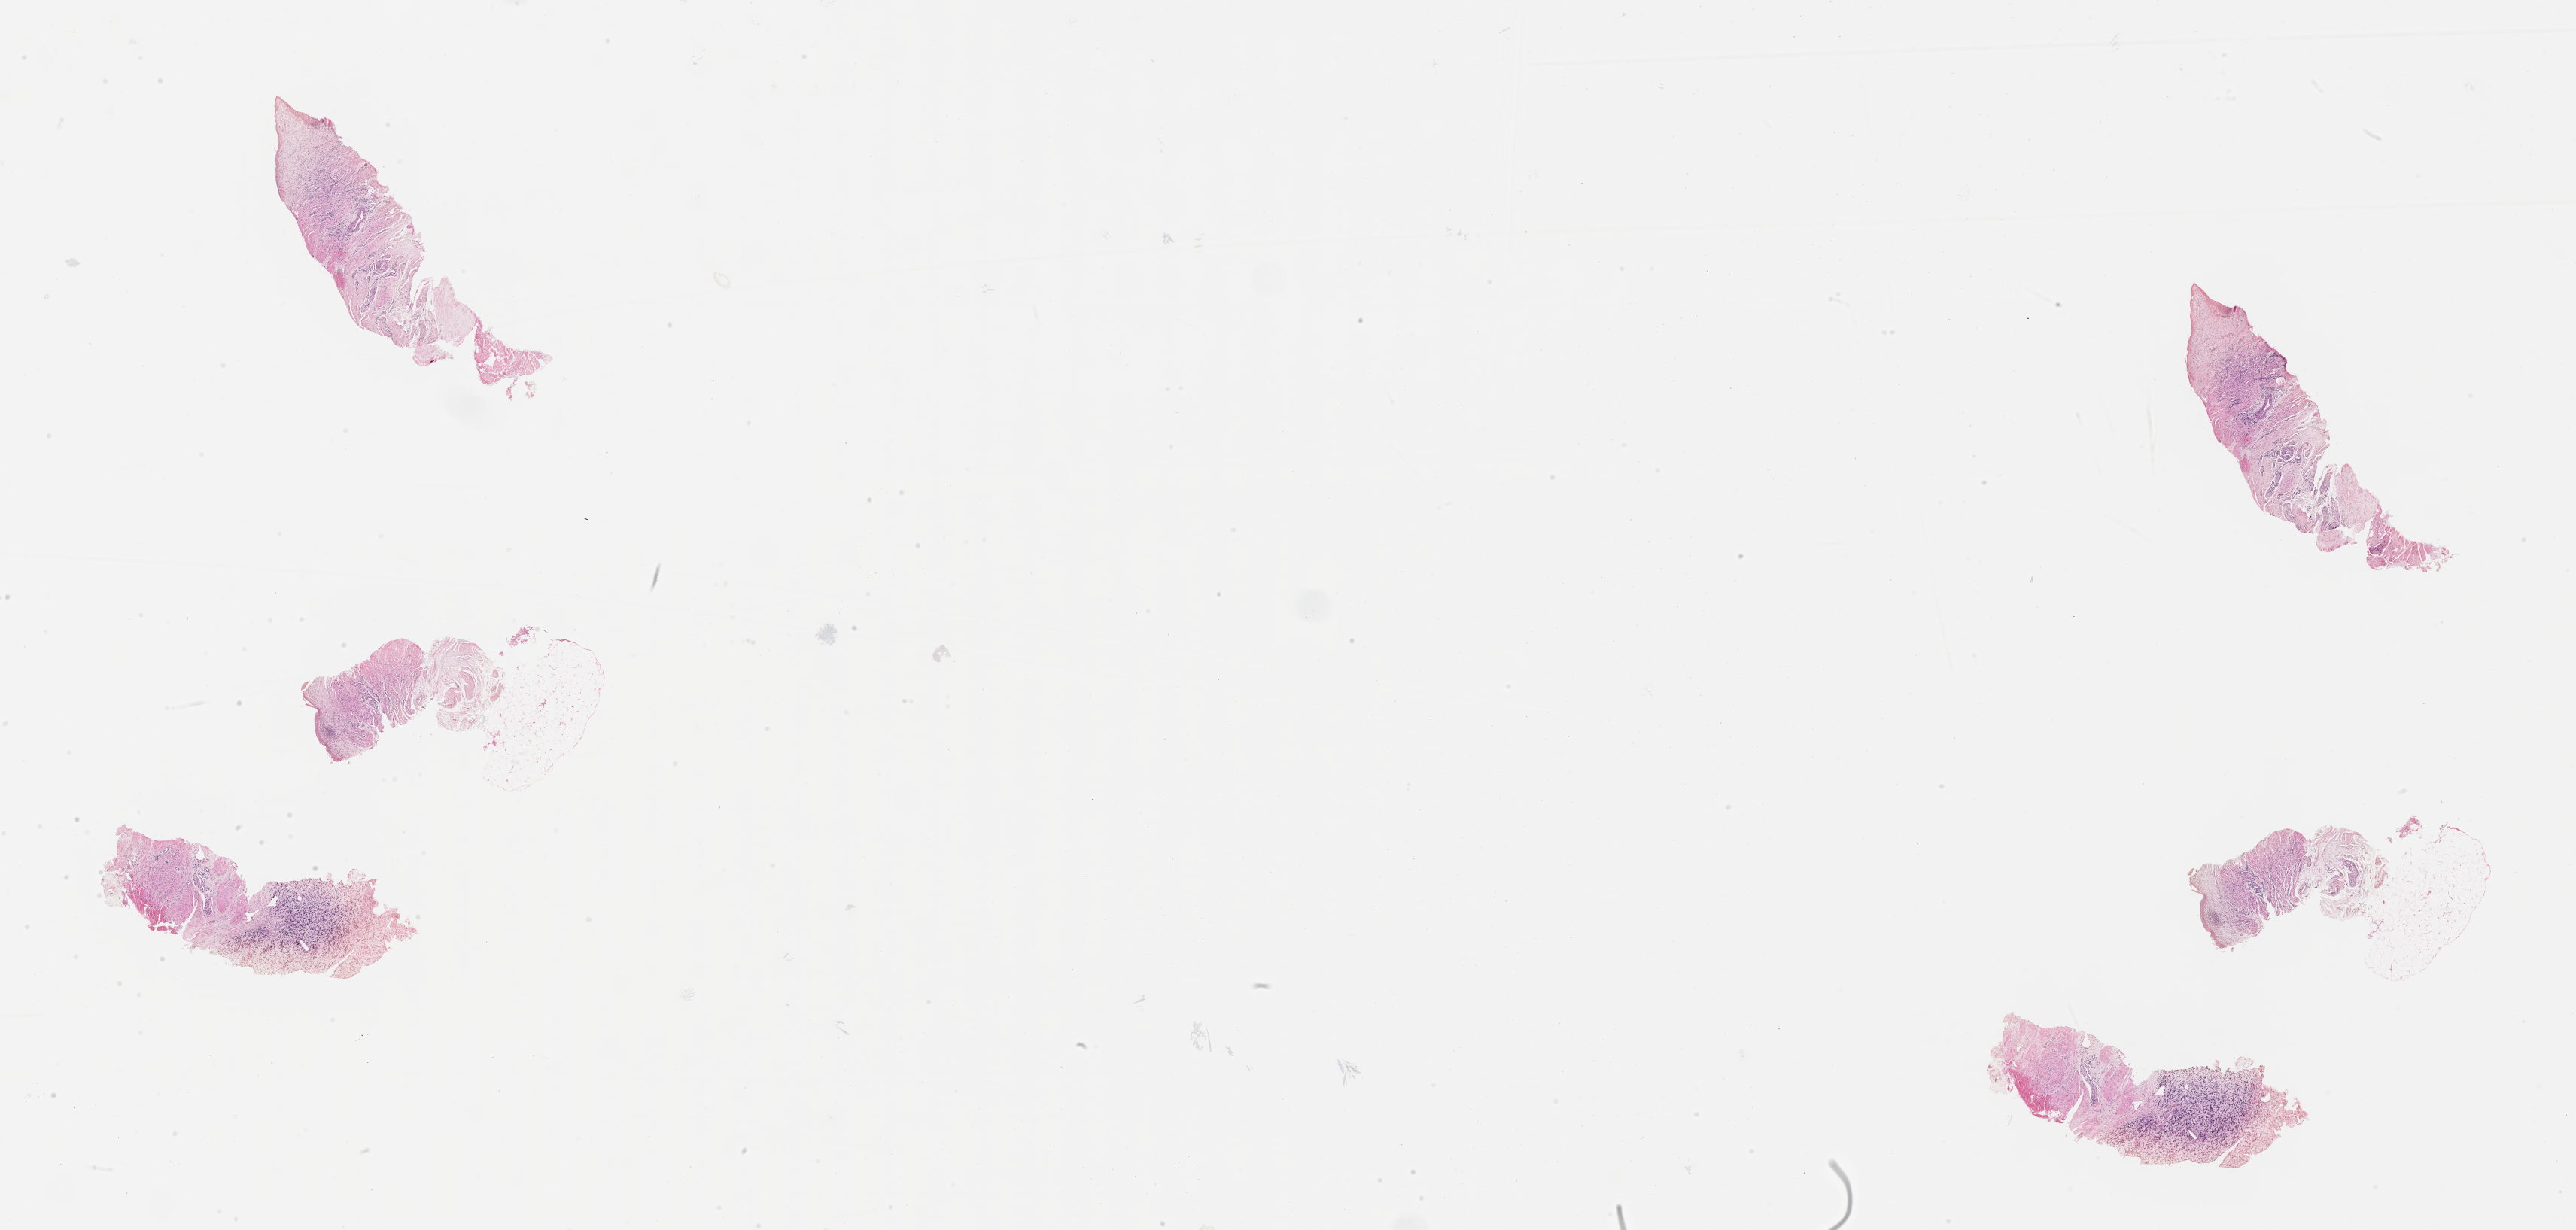
Whole-slide image, haematoxylin and eosin stain of tumor tissue — whole scanned area (about 27.7 x 13.2 mm) shown as a low-resolution overview. FFPE section. Sample anatomic site: pelvis. Female patient, age at diagnosis 2.0 years.
* diagnosis: rhabdomyosarcoma; histological classification: embryonal rhabdomyosarcoma
* metastatic status at presentation (as recorded): non-metastatic
* stage (as recorded): 1